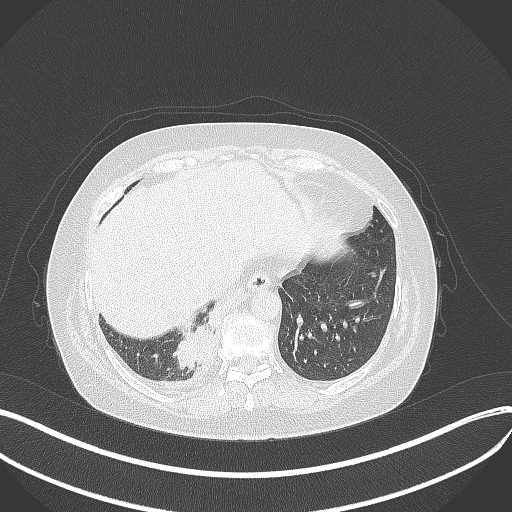
Chest CT, one axial slice. Slice 89 of 381 in the series (ordered by position). 120 kVp. Lung window (W 1500 / L -600 HU). 1 mm slice thickness. 512 × 512 image matrix. Patient: female, 56 years. From the clinical record (not read from this slice): clinical TNM (as recorded): T2b N1 M0.
Annotated regions visible in this slice (bounding box drawn by a radiologist):
- lung tumour (recorded histology: small cell carcinoma): bounding box [x1, y1, x2, y2] px = [169, 323, 219, 381]